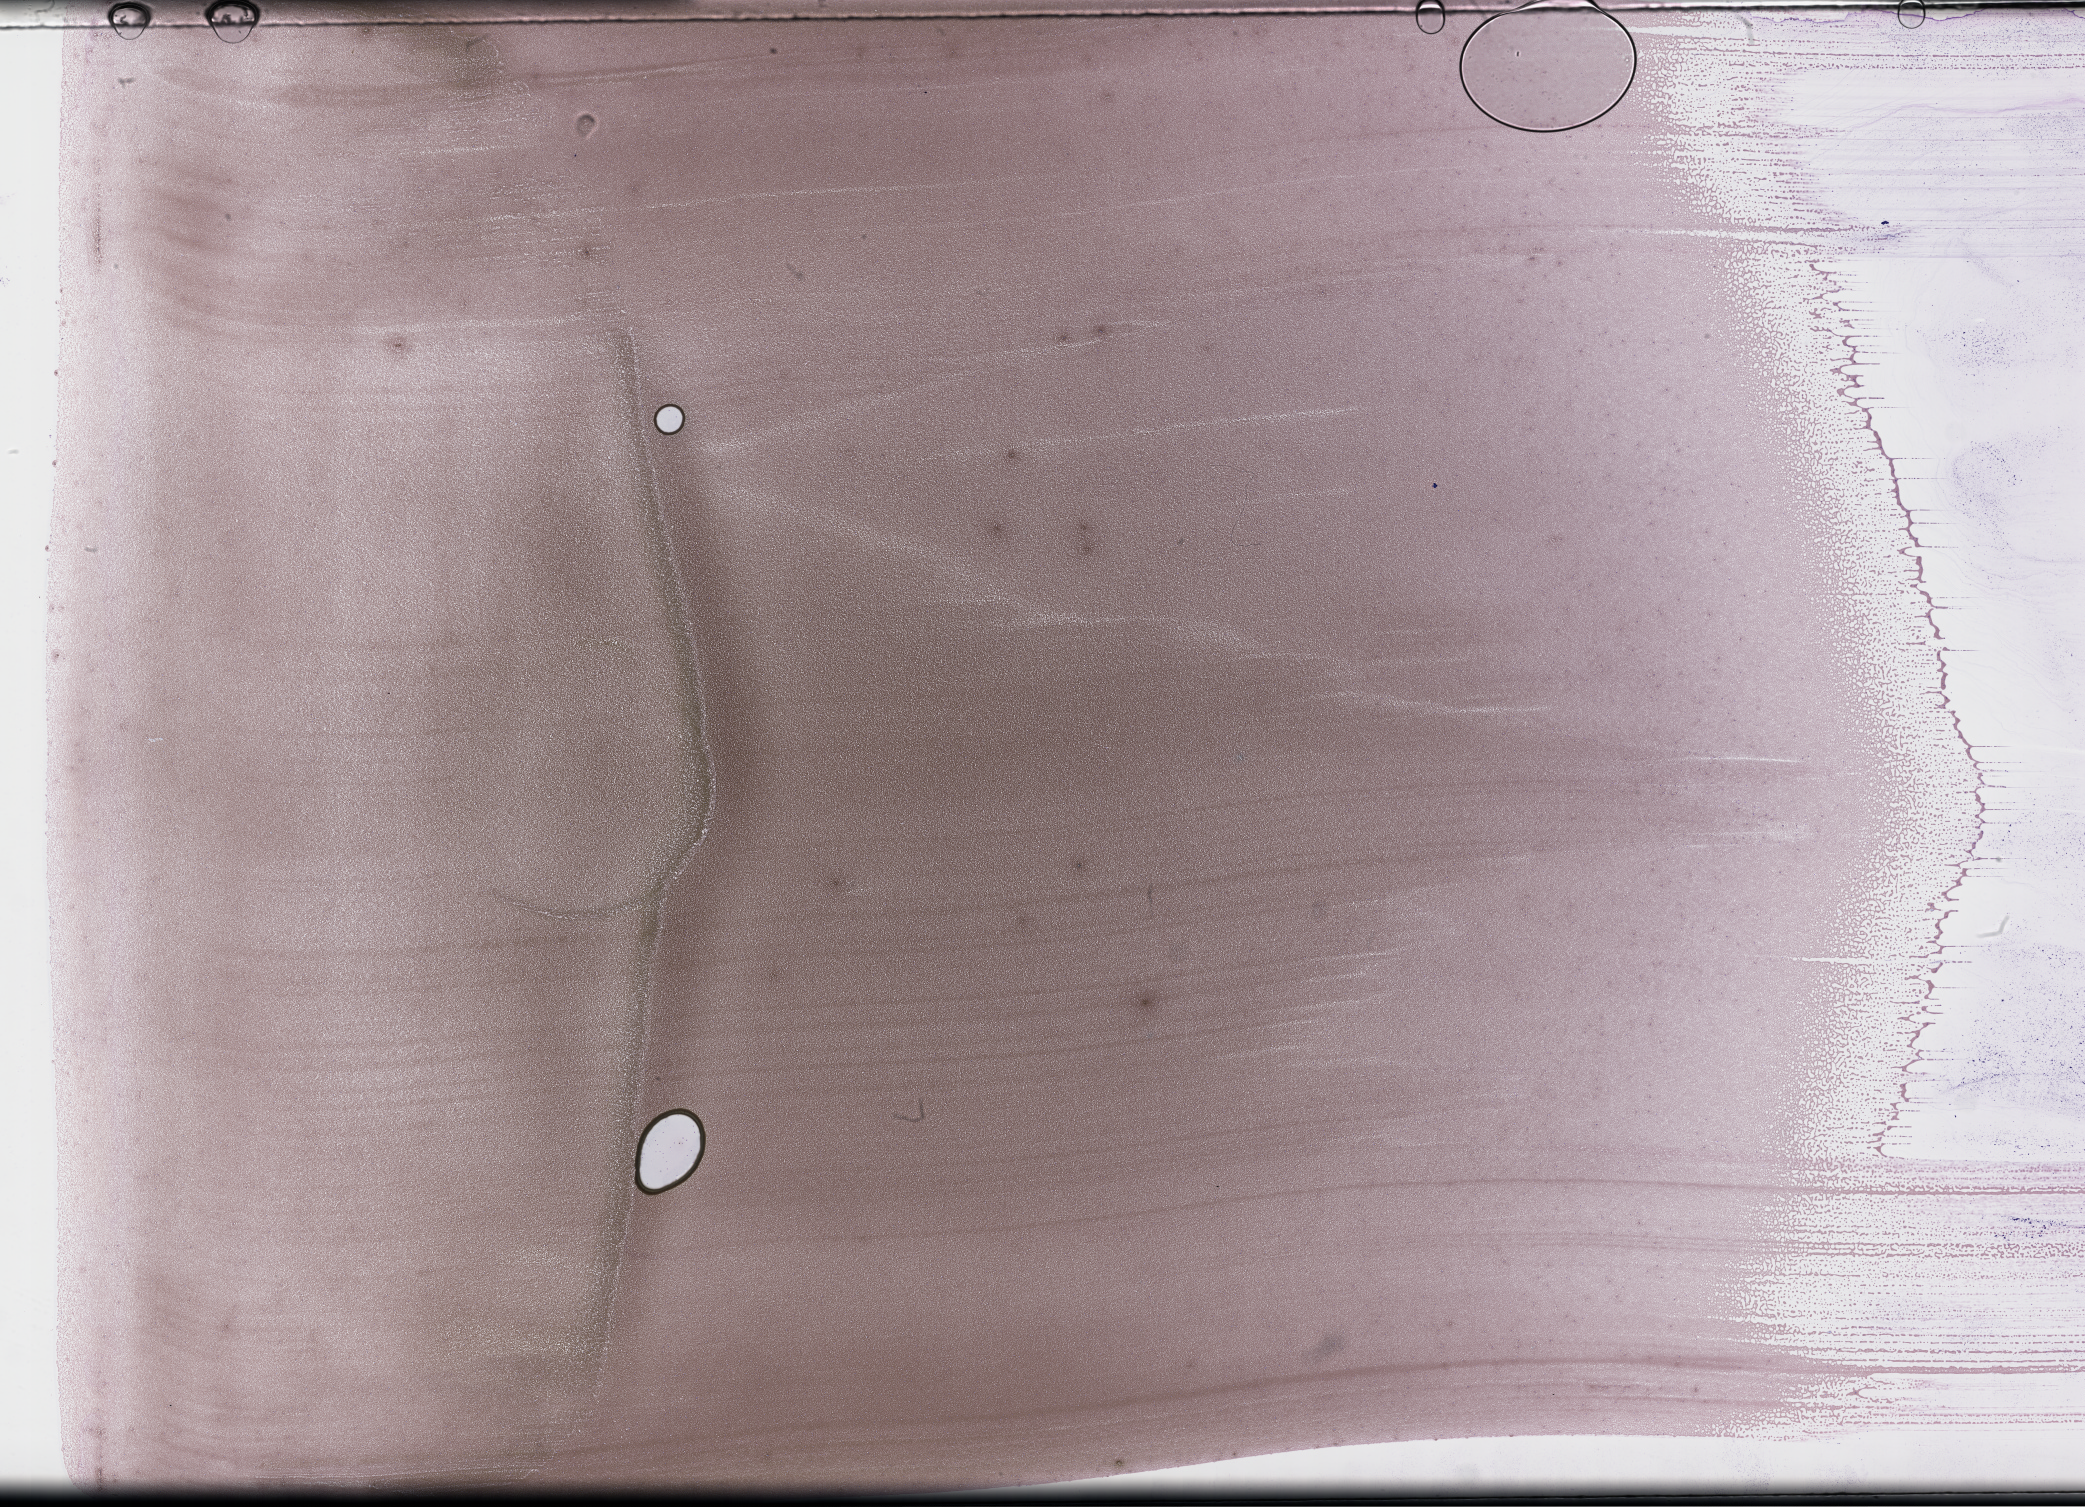
Wright-Giemsa-stained whole blood smear, whole-slide image, low-resolution overview of the scanned area, about 33.7 x 24.3 mm; EDTA-anticoagulated smear. Patient sex: male.
From a patient with: Plasma Cell Myeloma.